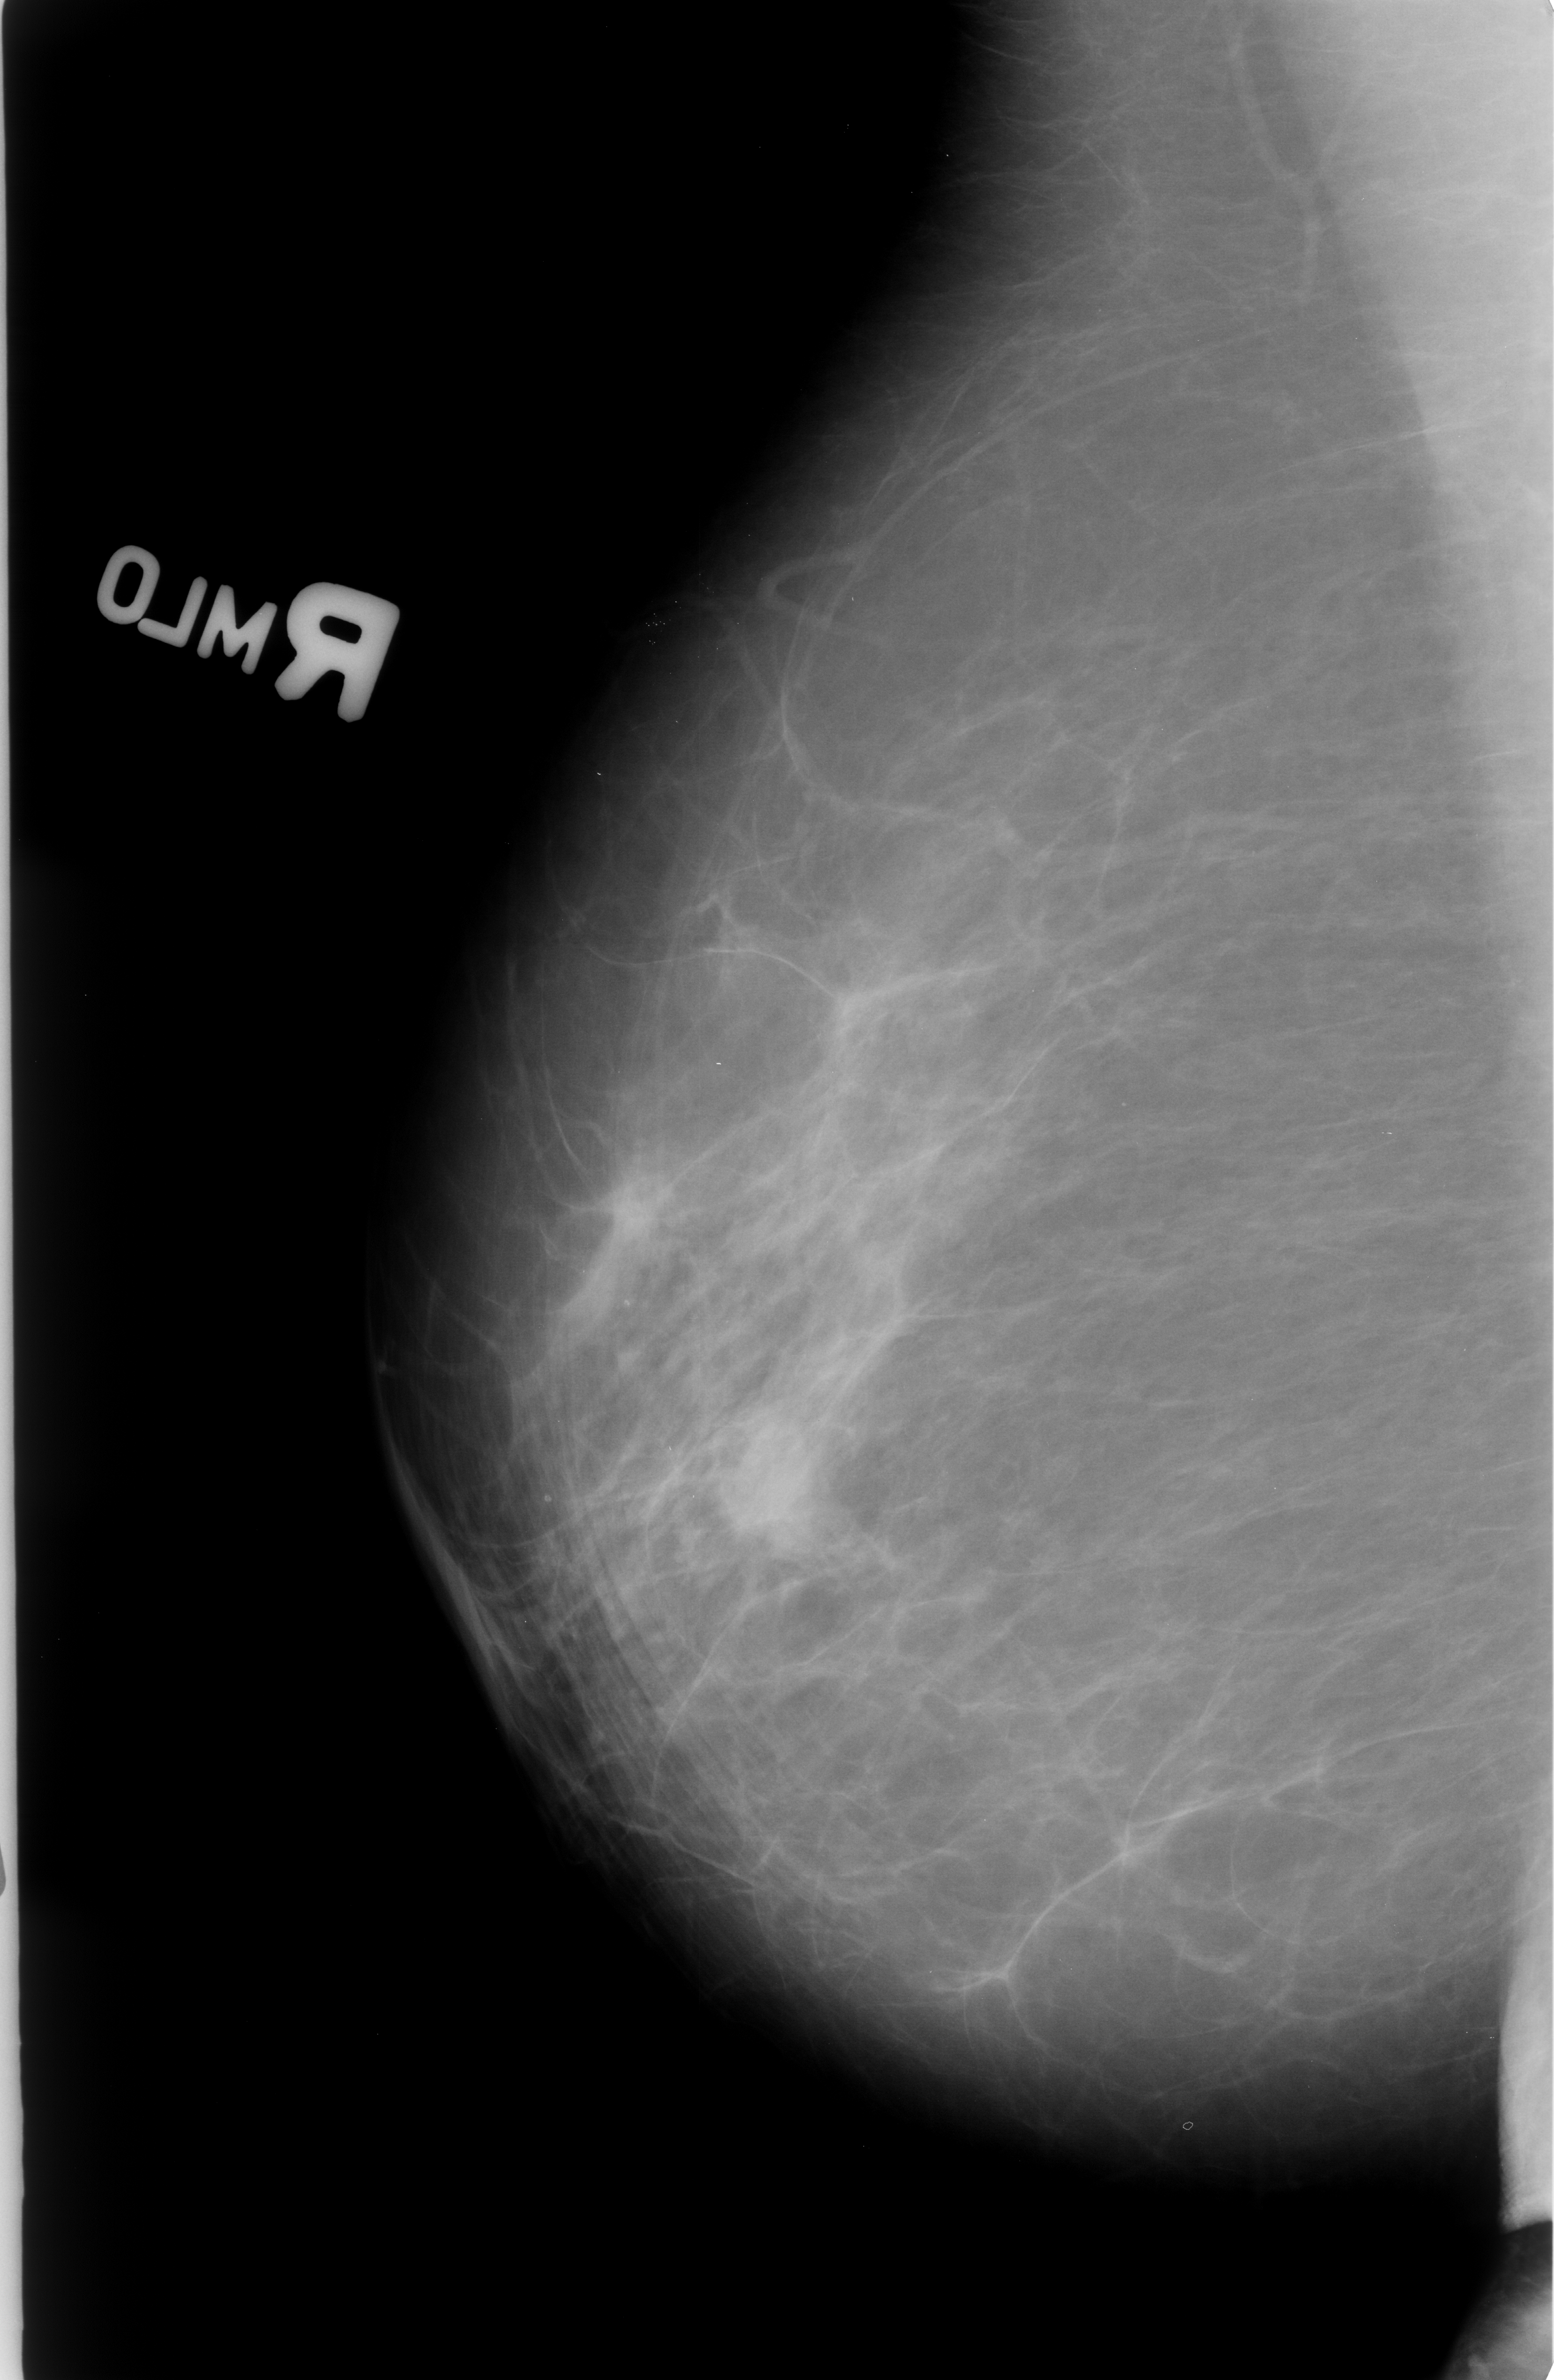
Mammogram (digitized film); right breast; mediolateral oblique (MLO) view.
Abnormality record for this image: mass, shape irregular, margins spiculated; BI-RADS assessment category 5; pathology (as recorded): malignant.